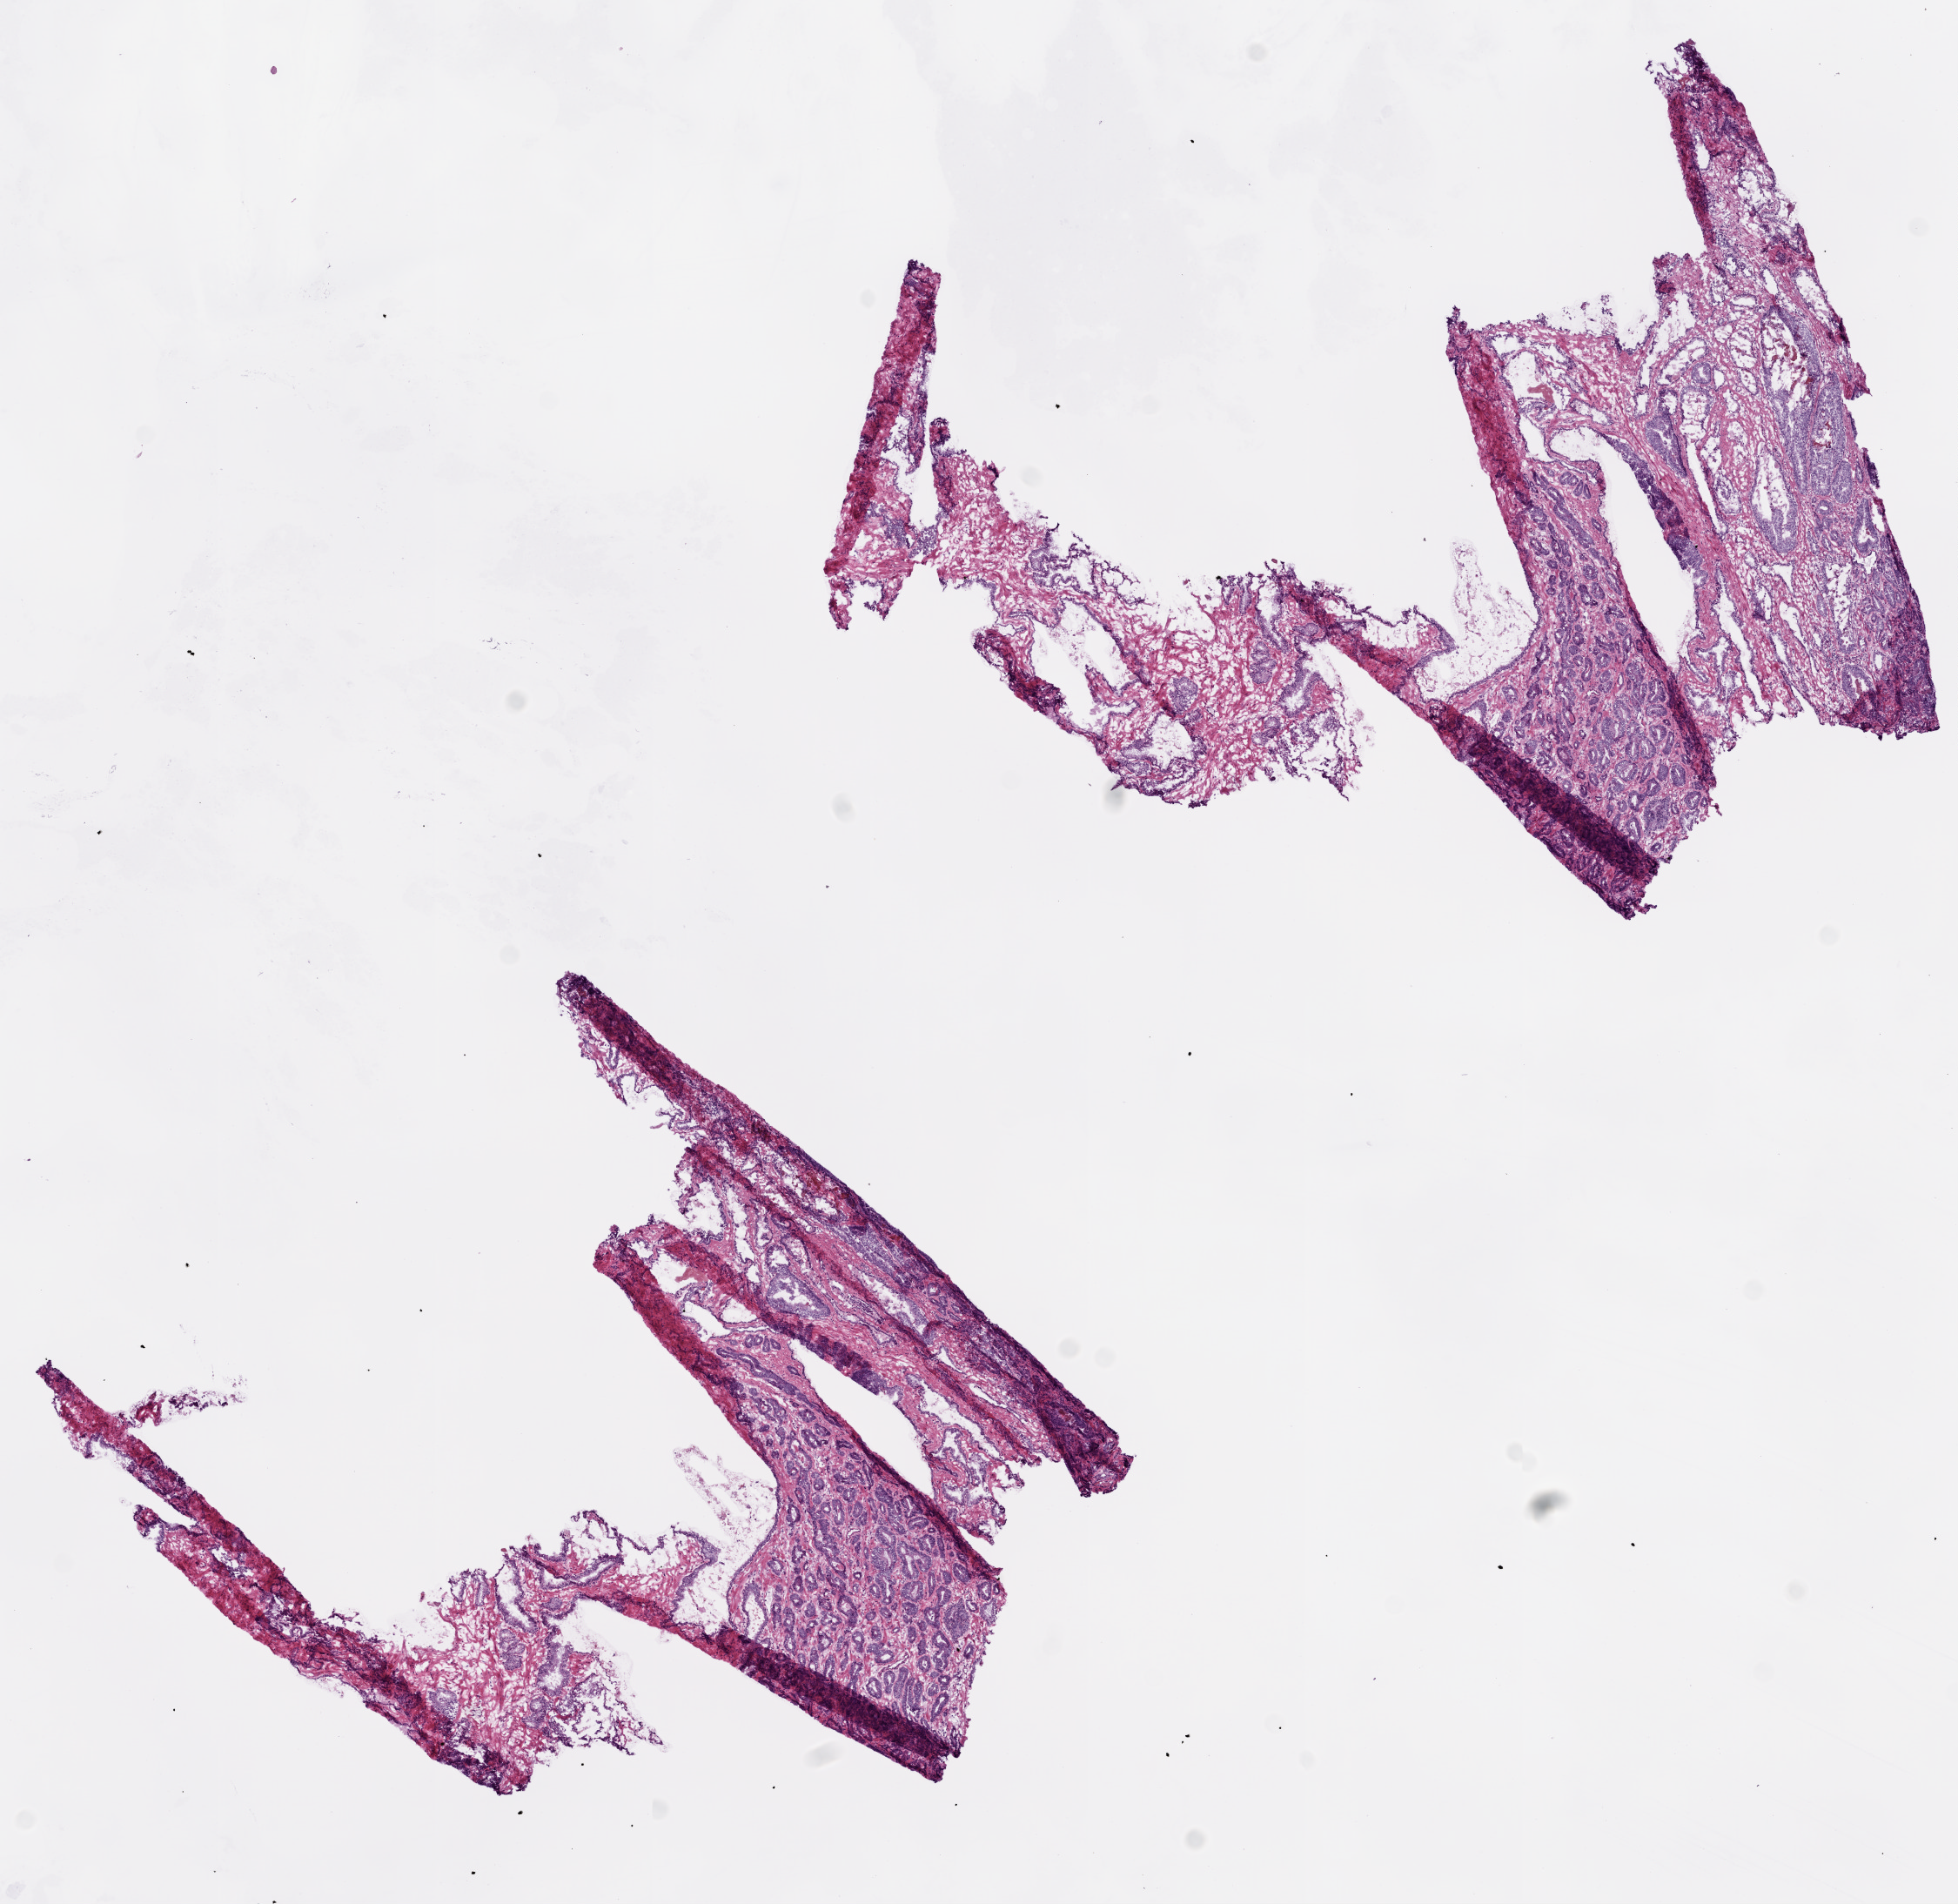
Digitized H&E-stained tissue section (whole slide) — low-resolution overview of the scanned area, about 9.0 x 8.8 mm (slide scanned at 20x); frozen section; sample: primary tumour, prostate. Male patient; age at initial diagnosis 72 years. Gleason score: 6 (2+4). Slide review estimates, as recorded: tumour cells 35%, tumour nuclei 35%, normal cells 45%, stromal cells 20%, necrosis 0%. Infiltration values recorded for this section: lymphocyte infiltration 0%, monocyte infiltration 0%, neutrophil infiltration 0%.
Pathologic diagnosis: Acinar cell carcinoma (prostate gland). Laterality: bilateral.